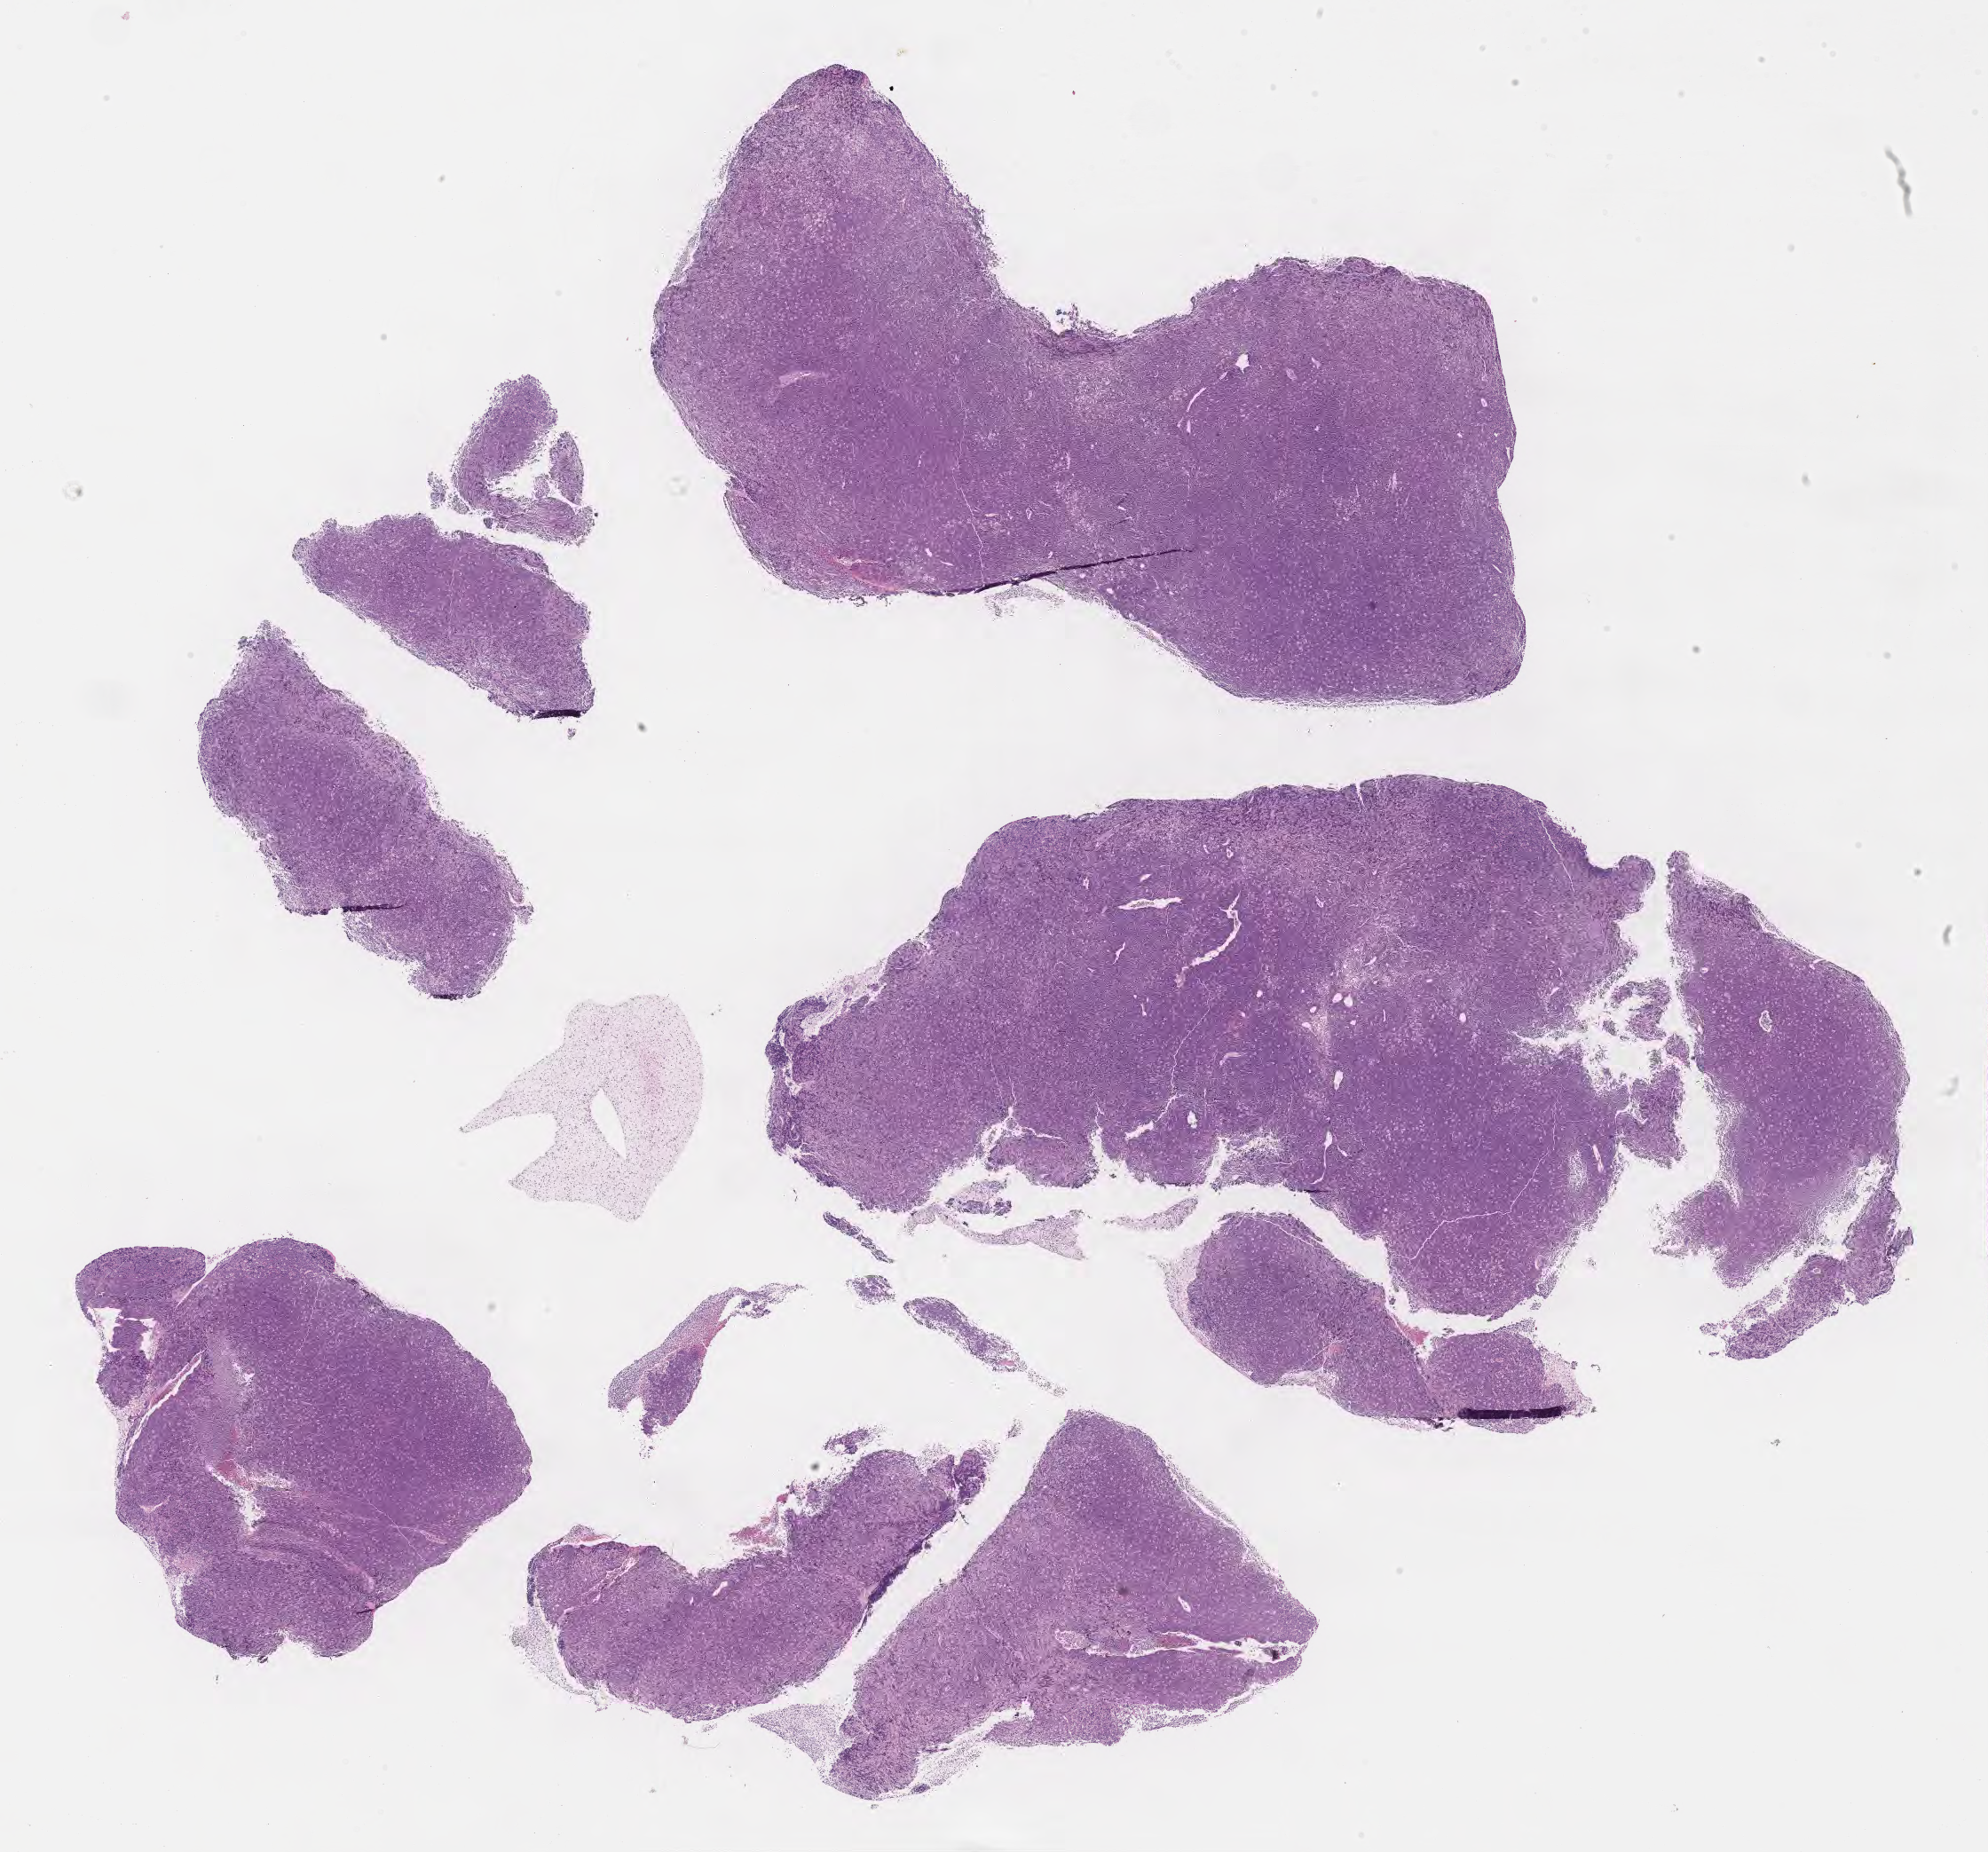
Digitized H&E-stained section — whole scanned area (about 18.1 x 16.9 mm) shown as a low-resolution overview; specimen: tumor tissue; site: soft tissue. Female, age 9 years at initial diagnosis.
• histologic diagnosis: Burkitt lymphoma, NOS